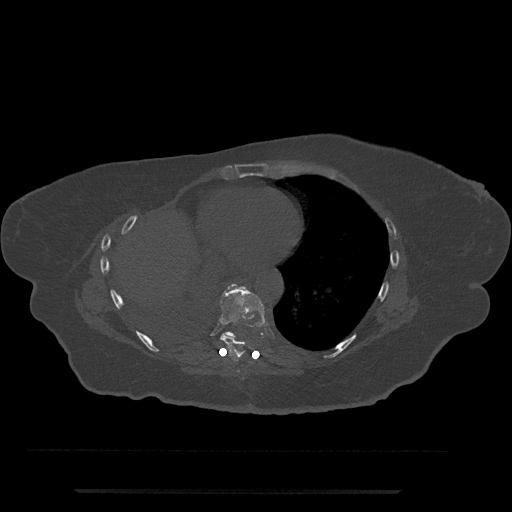
CT including the spine, one axial slice. Slice 379 of 797 in the series (ordered by position). Reconstruction kernel Br40s/3. Bone window (W 1800 / L 400 HU). 0.5 mm slice thickness. 512 × 512 image matrix. Patient: female, 51 years. Case-level facts recorded for this patient, not image findings: primary cancer: neuro; vertebrae with lytic lesions (as recorded): T8.
Annotated regions visible in this slice (semi-automatic segmentation, software-assisted and operator-edited):
- T7 vertebra: bounding box (x1, y1, x2, y2) in pixels: (237, 370, 240, 373)
- T8 vertebra: (220, 283, 265, 359)
- T9 vertebra: (224, 286, 264, 340)